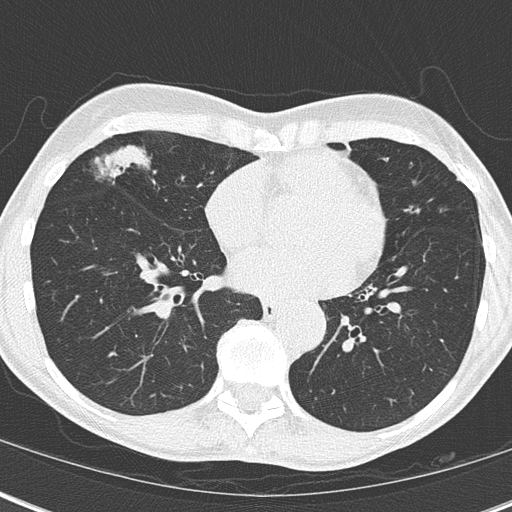
Axial slice from a low-dose chest CT screening exam; third annual screen; lung window (W 1500 / L -600 HU); slice 105 of 173 in the series. Female participant, aged 67 years at enrolment. Current smoker at enrolment.
Expert-annotated lung lesion, bounding box <92,139,189,221> (left, top, right, bottom; pixels). Reader record for this screening exam (exam-level; its link to the box is not recorded): non-calcified nodule or mass ≥4 mm, right middle lobe, 32 × 17 mm, mixed attenuation, pre-existing on the prior screen: yes; interval growth: yes. Official screen result: positive, other. Later outcome: lung cancer diagnosed 76 days after this screen — bronchiolo-alveolar adenocarcinoma, NOS, right middle lobe, well differentiated (G1), stage IA (AJCC 6th edition), 25 mm at pathology.